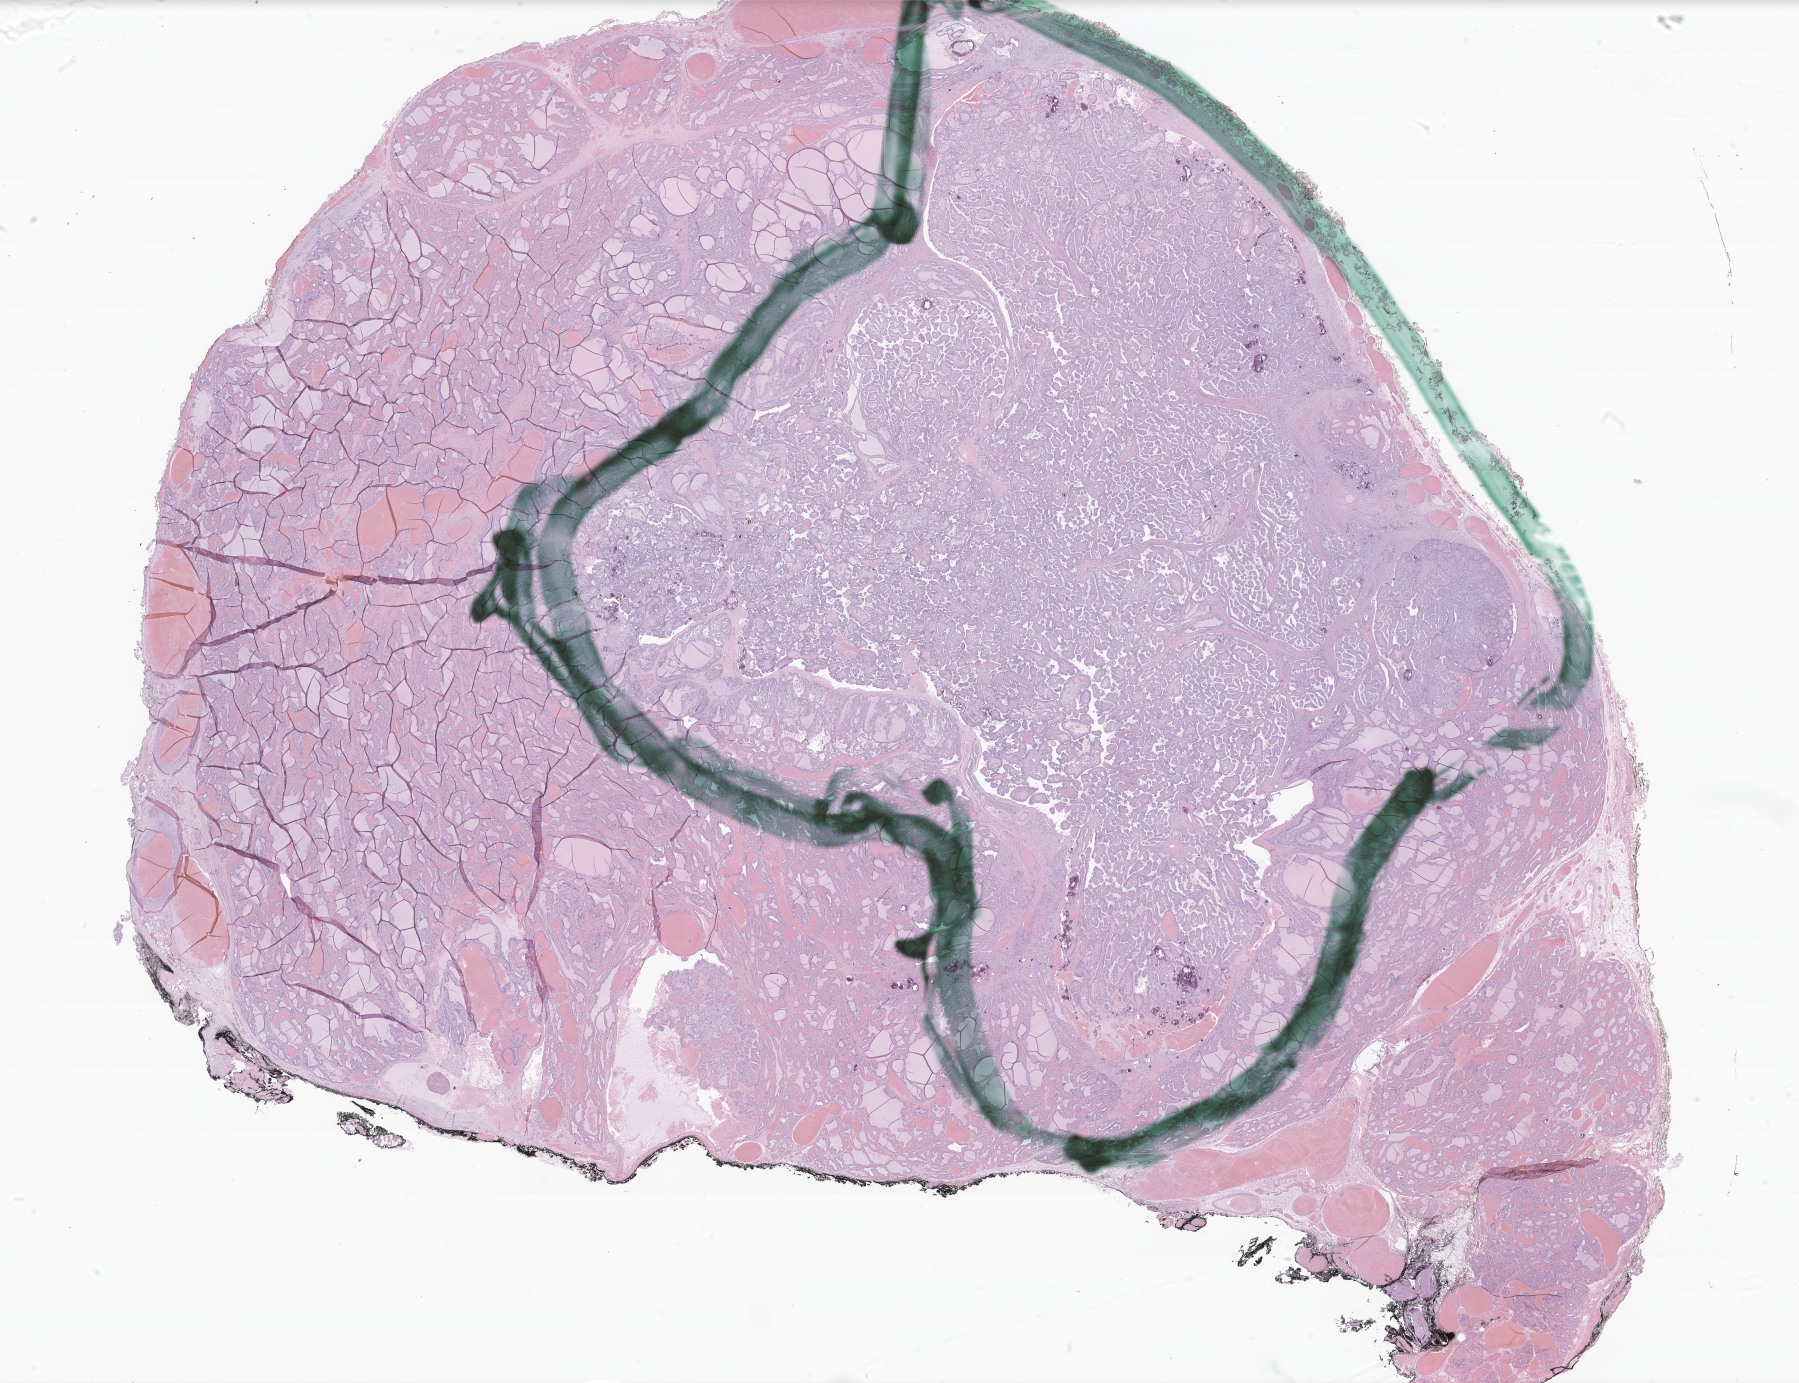
H&E whole-slide image of tumor tissue from the thyroid — low-resolution overview of the scanned area, about 30.3 x 23.3 mm; FFPE section. Female patient, age 201 months (16 years 9 months).
Diagnosis: Papillary carcinoma, NOS.